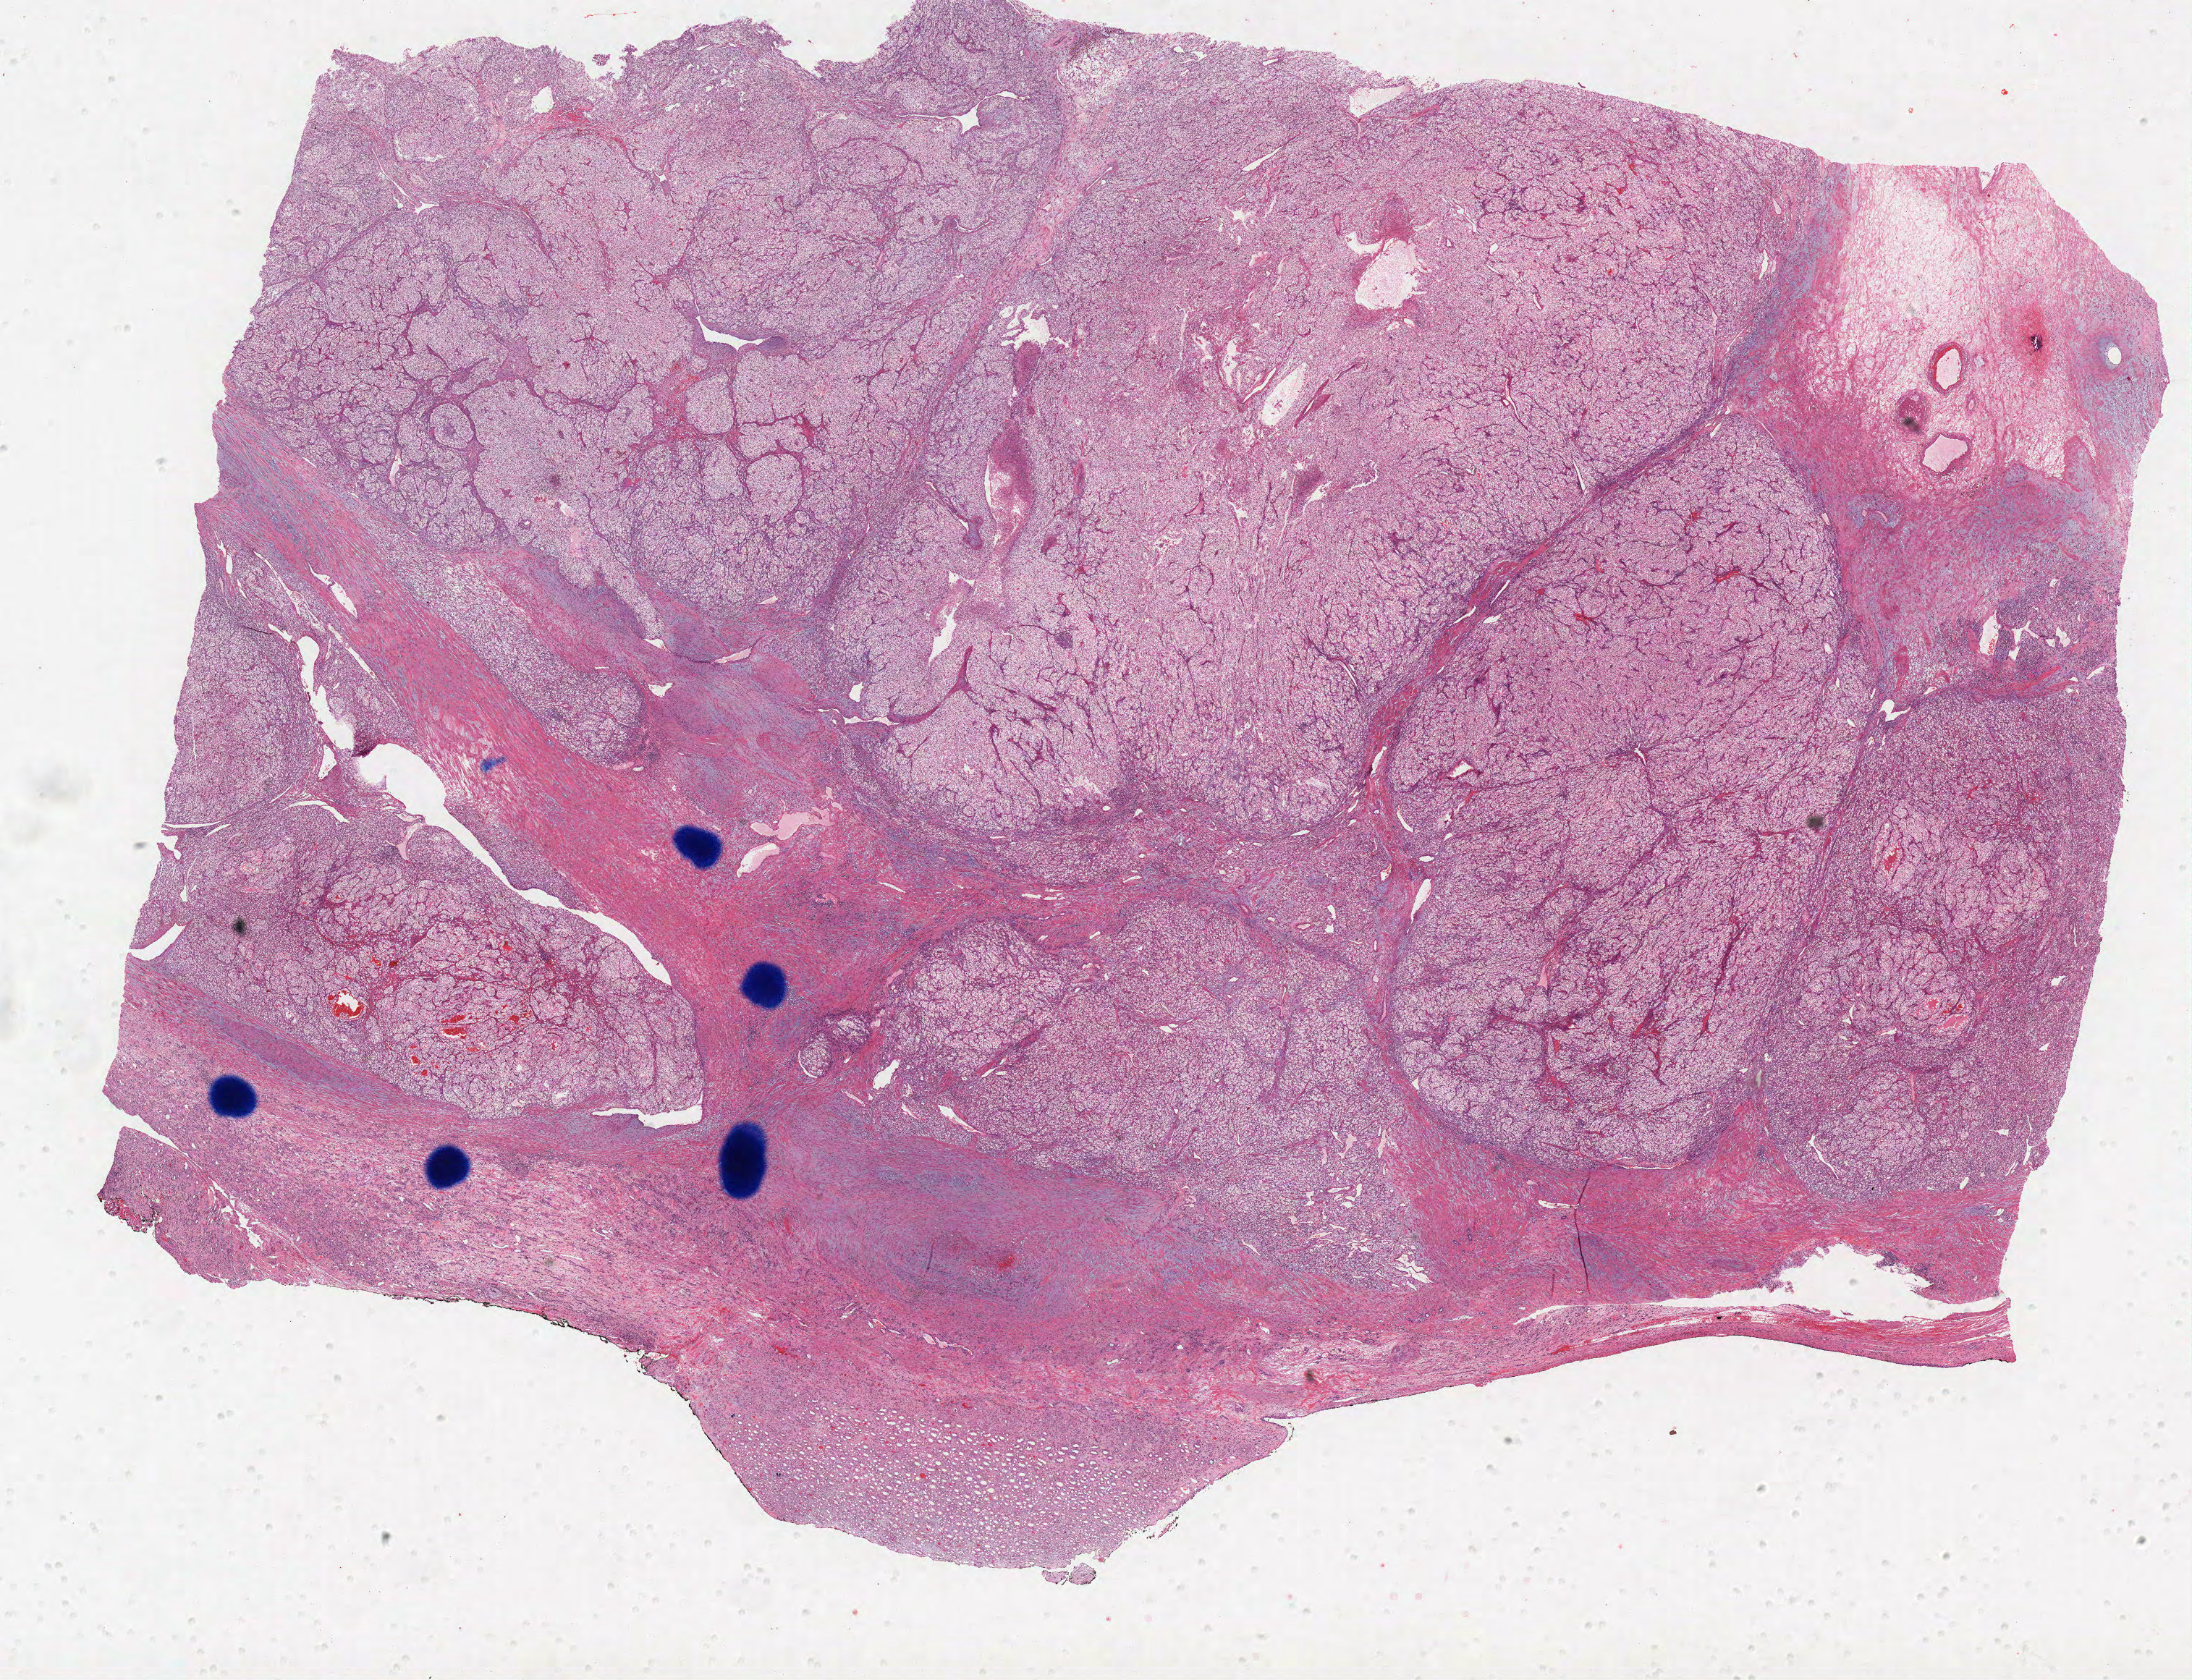
H&E whole-slide image — whole scanned area (about 24.2 x 18.6 mm) shown as a low-resolution overview; formalin-fixed paraffin-embedded (FFPE) diagnostic section; kidney, primary tumour sample. Male patient; age at initial diagnosis 52 years. Histologic grade: G3 (poorly differentiated).
AJCC pathologic stage: I. TNM: T1b NX M0. Diagnosis: Clear cell adenocarcinoma, NOS.